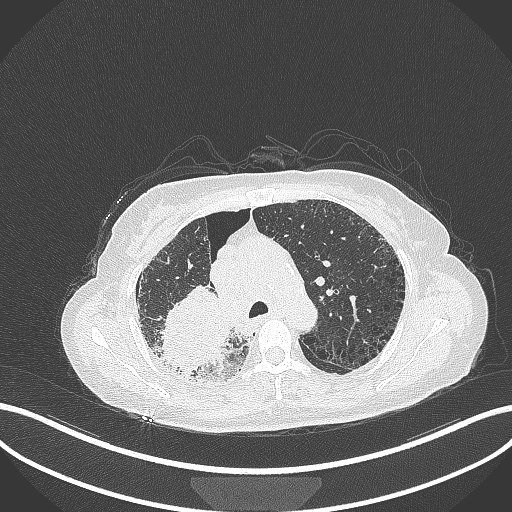
Chest CT, one axial slice; slice 242 of 408 in the series (ordered by position); reconstruction kernel B70f; lung window (W 1500 / L -600 HU); 1 mm slice thickness; 512 × 512 image matrix, field of view 400 × 400 mm. Female patient, age 64 years. From the clinical record (not read from this slice): clinical TNM (as recorded): T3 N3 M0.
Outlined on this slice (rectangle marked by the reading radiologist):
- lung tumour (recorded histology: squamous cell carcinoma): bounding box [x1, y1, x2, y2] px = [158, 284, 233, 378]